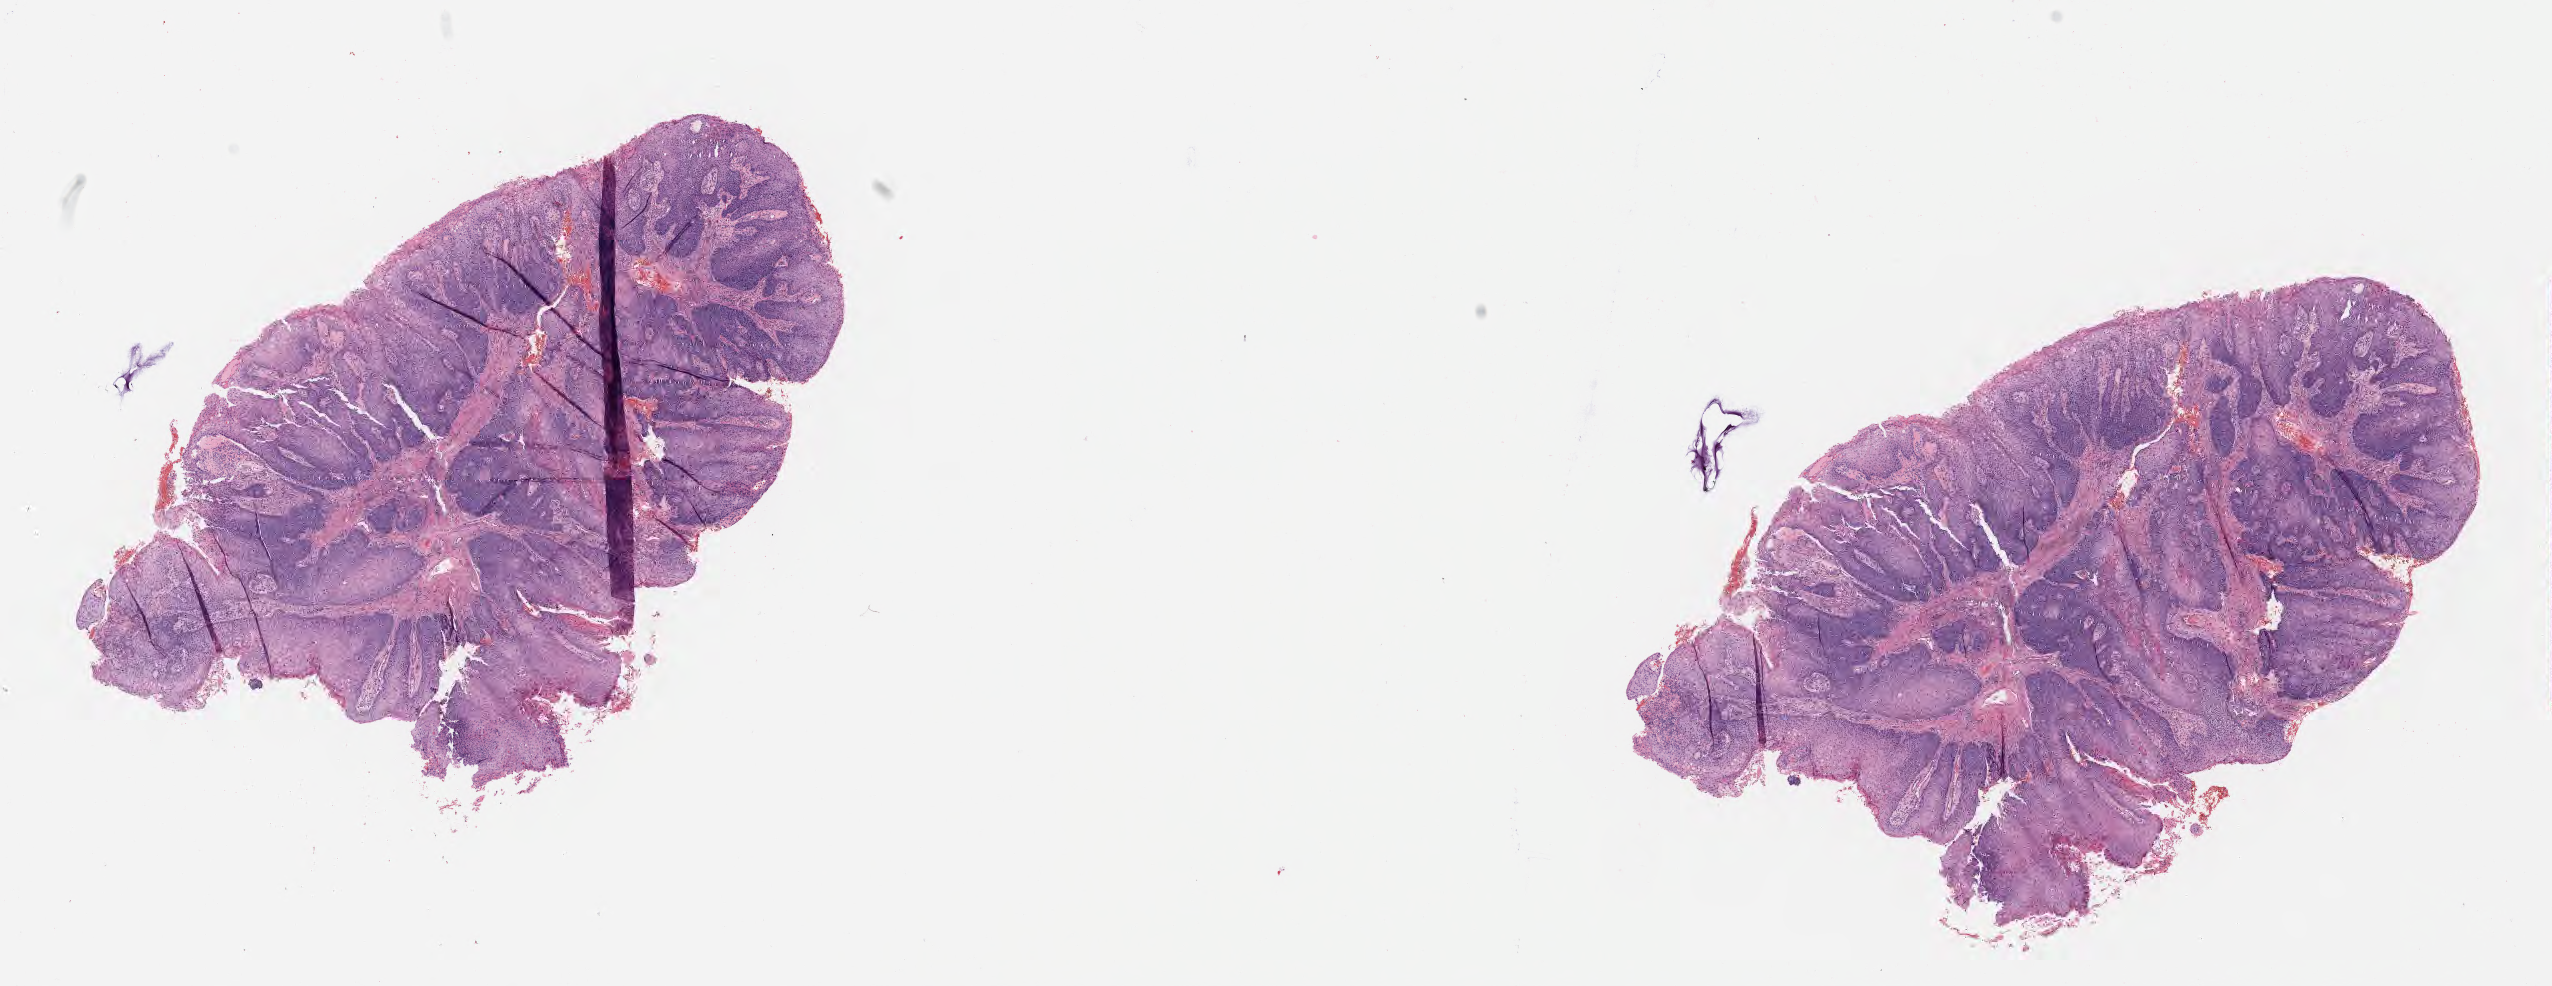
Whole-slide image, haematoxylin and eosin stain — a low-resolution overview of the entire scanned area, about 20.6 x 8.0 mm. Tumor tissue. Anatomic site: cervix. Female patient, aged 54.
Histologic diagnosis: Squamous cell carcinoma, large cell, nonkeratinizing, NOS.